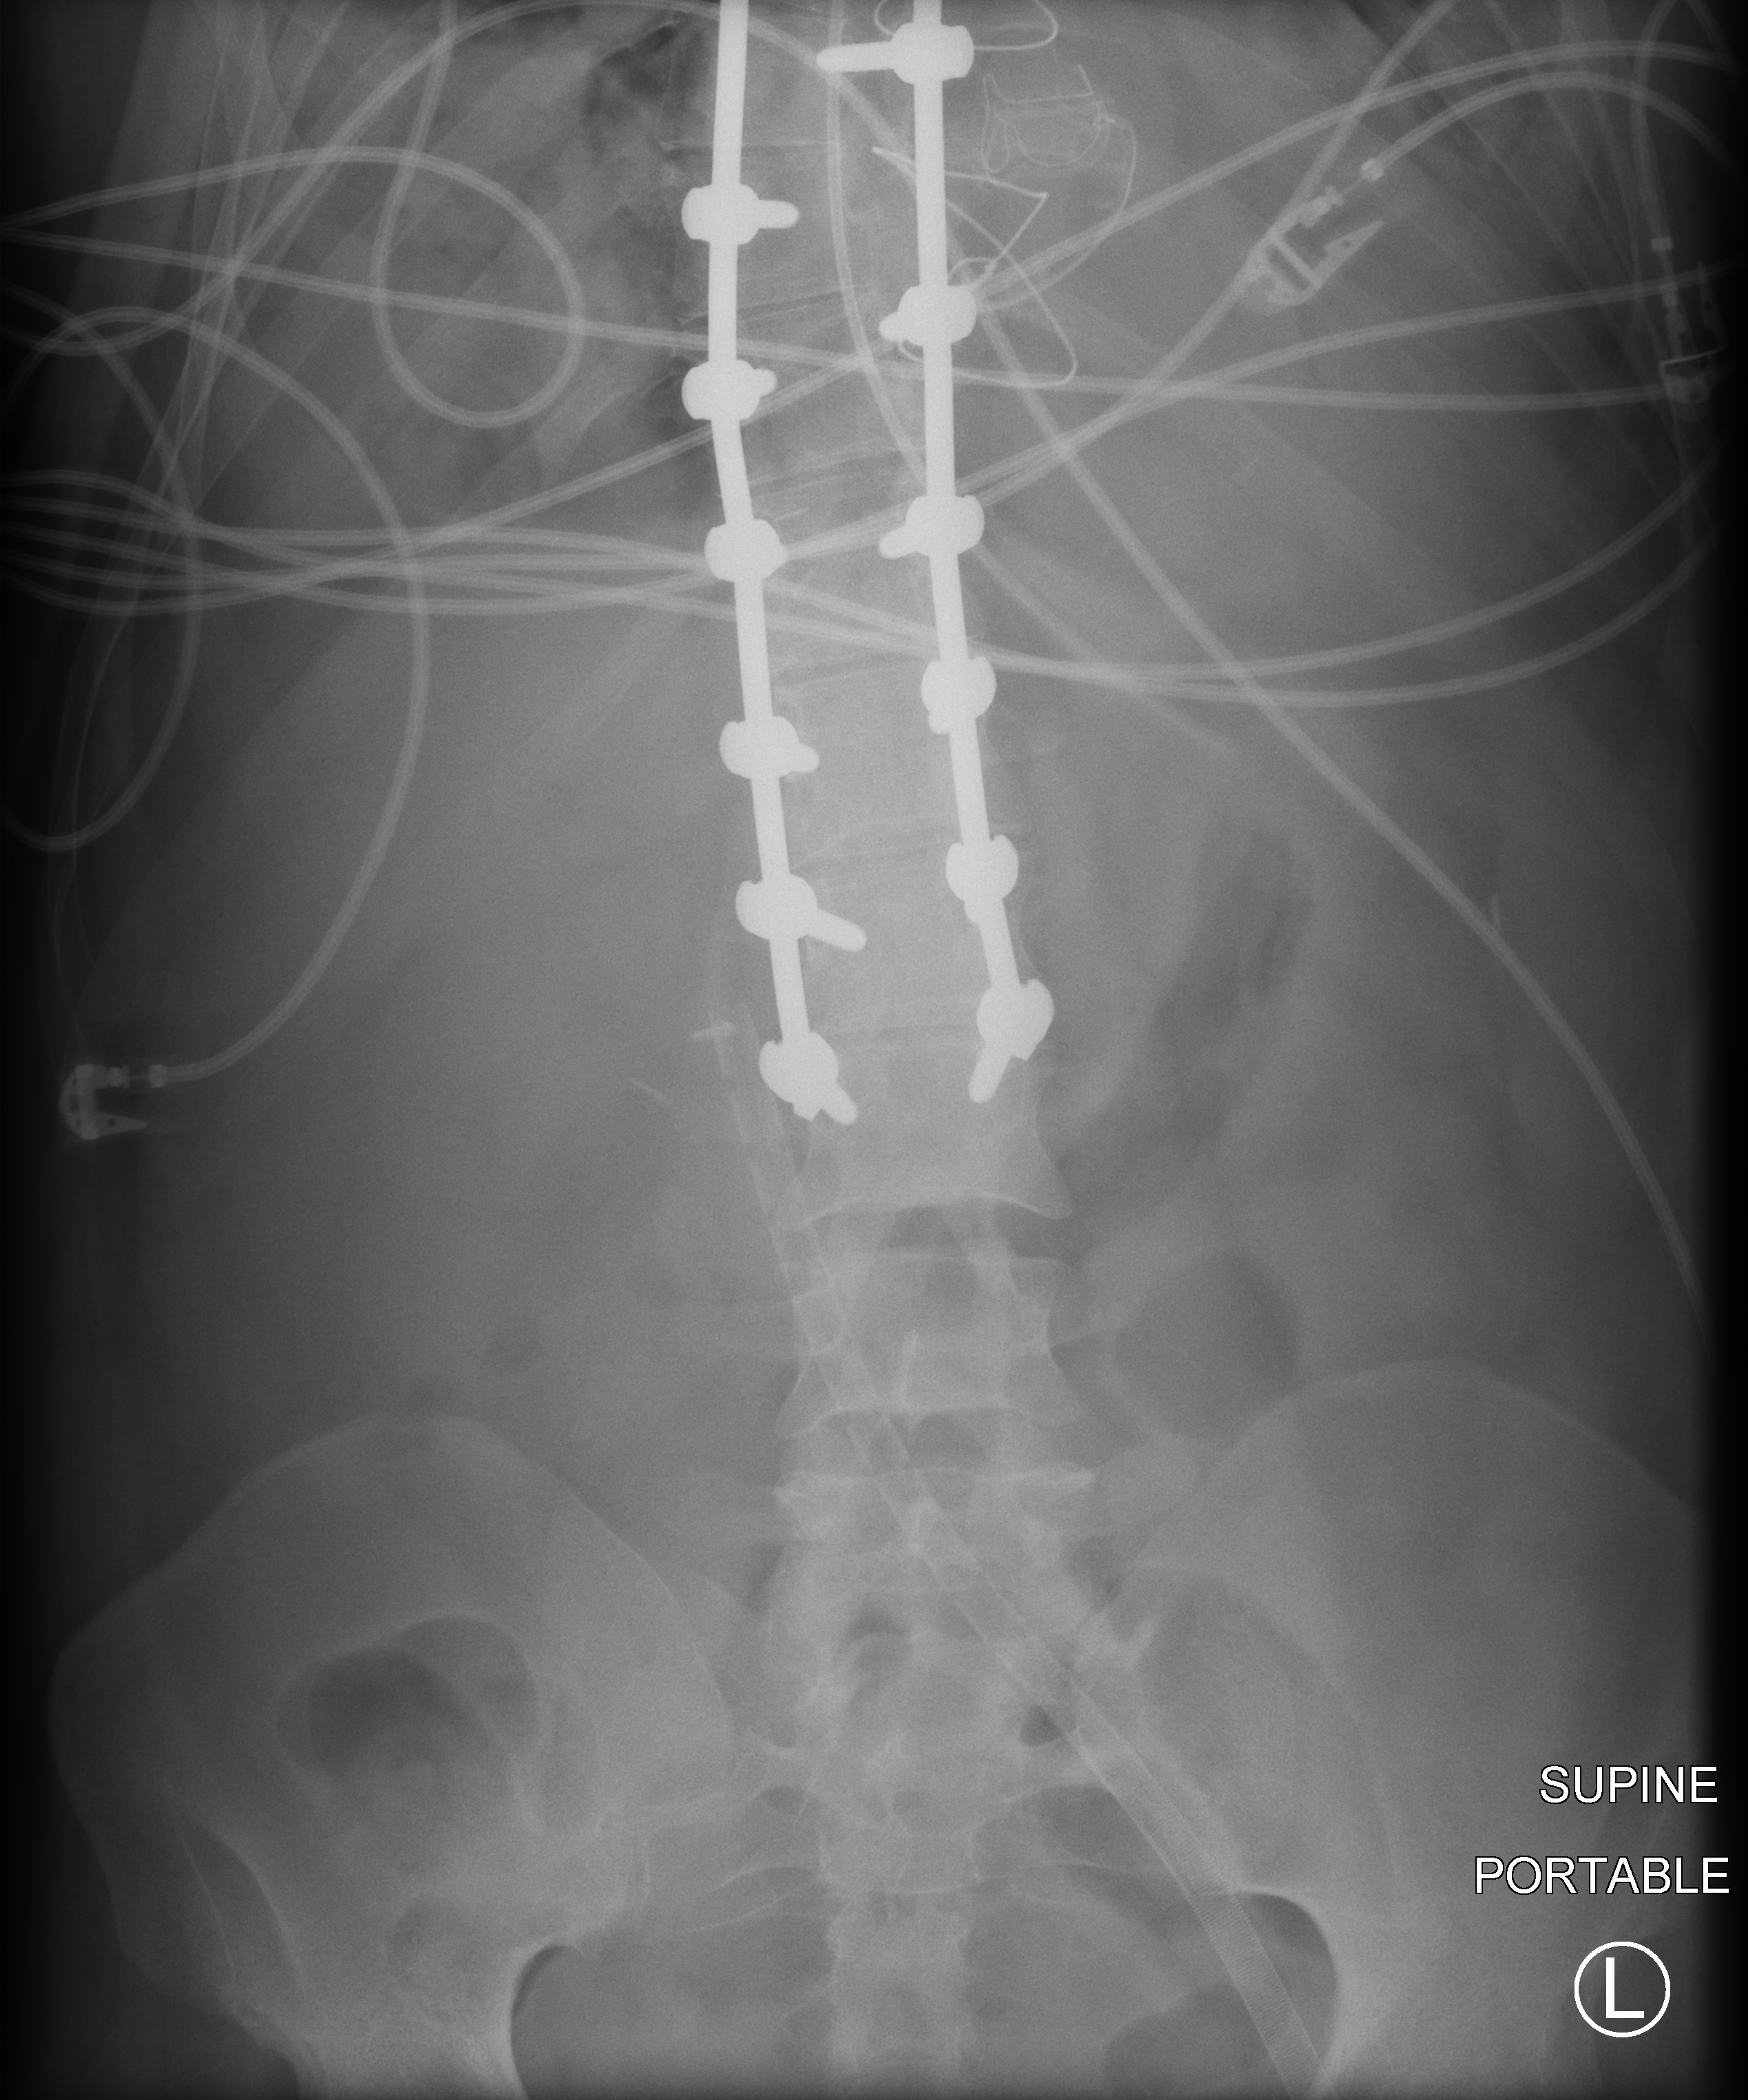
Bedside abdomen radiograph (computed radiography); anteroposterior (AP) projection. Adult patient hospitalised with COVID-19, age 18–59 years.
From the hospital-stay record, not from the radiograph (when in the stay this image was taken is not recorded):
- mechanically ventilated during this hospital stay: yes
- admitted to intensive care during this hospital stay: yes